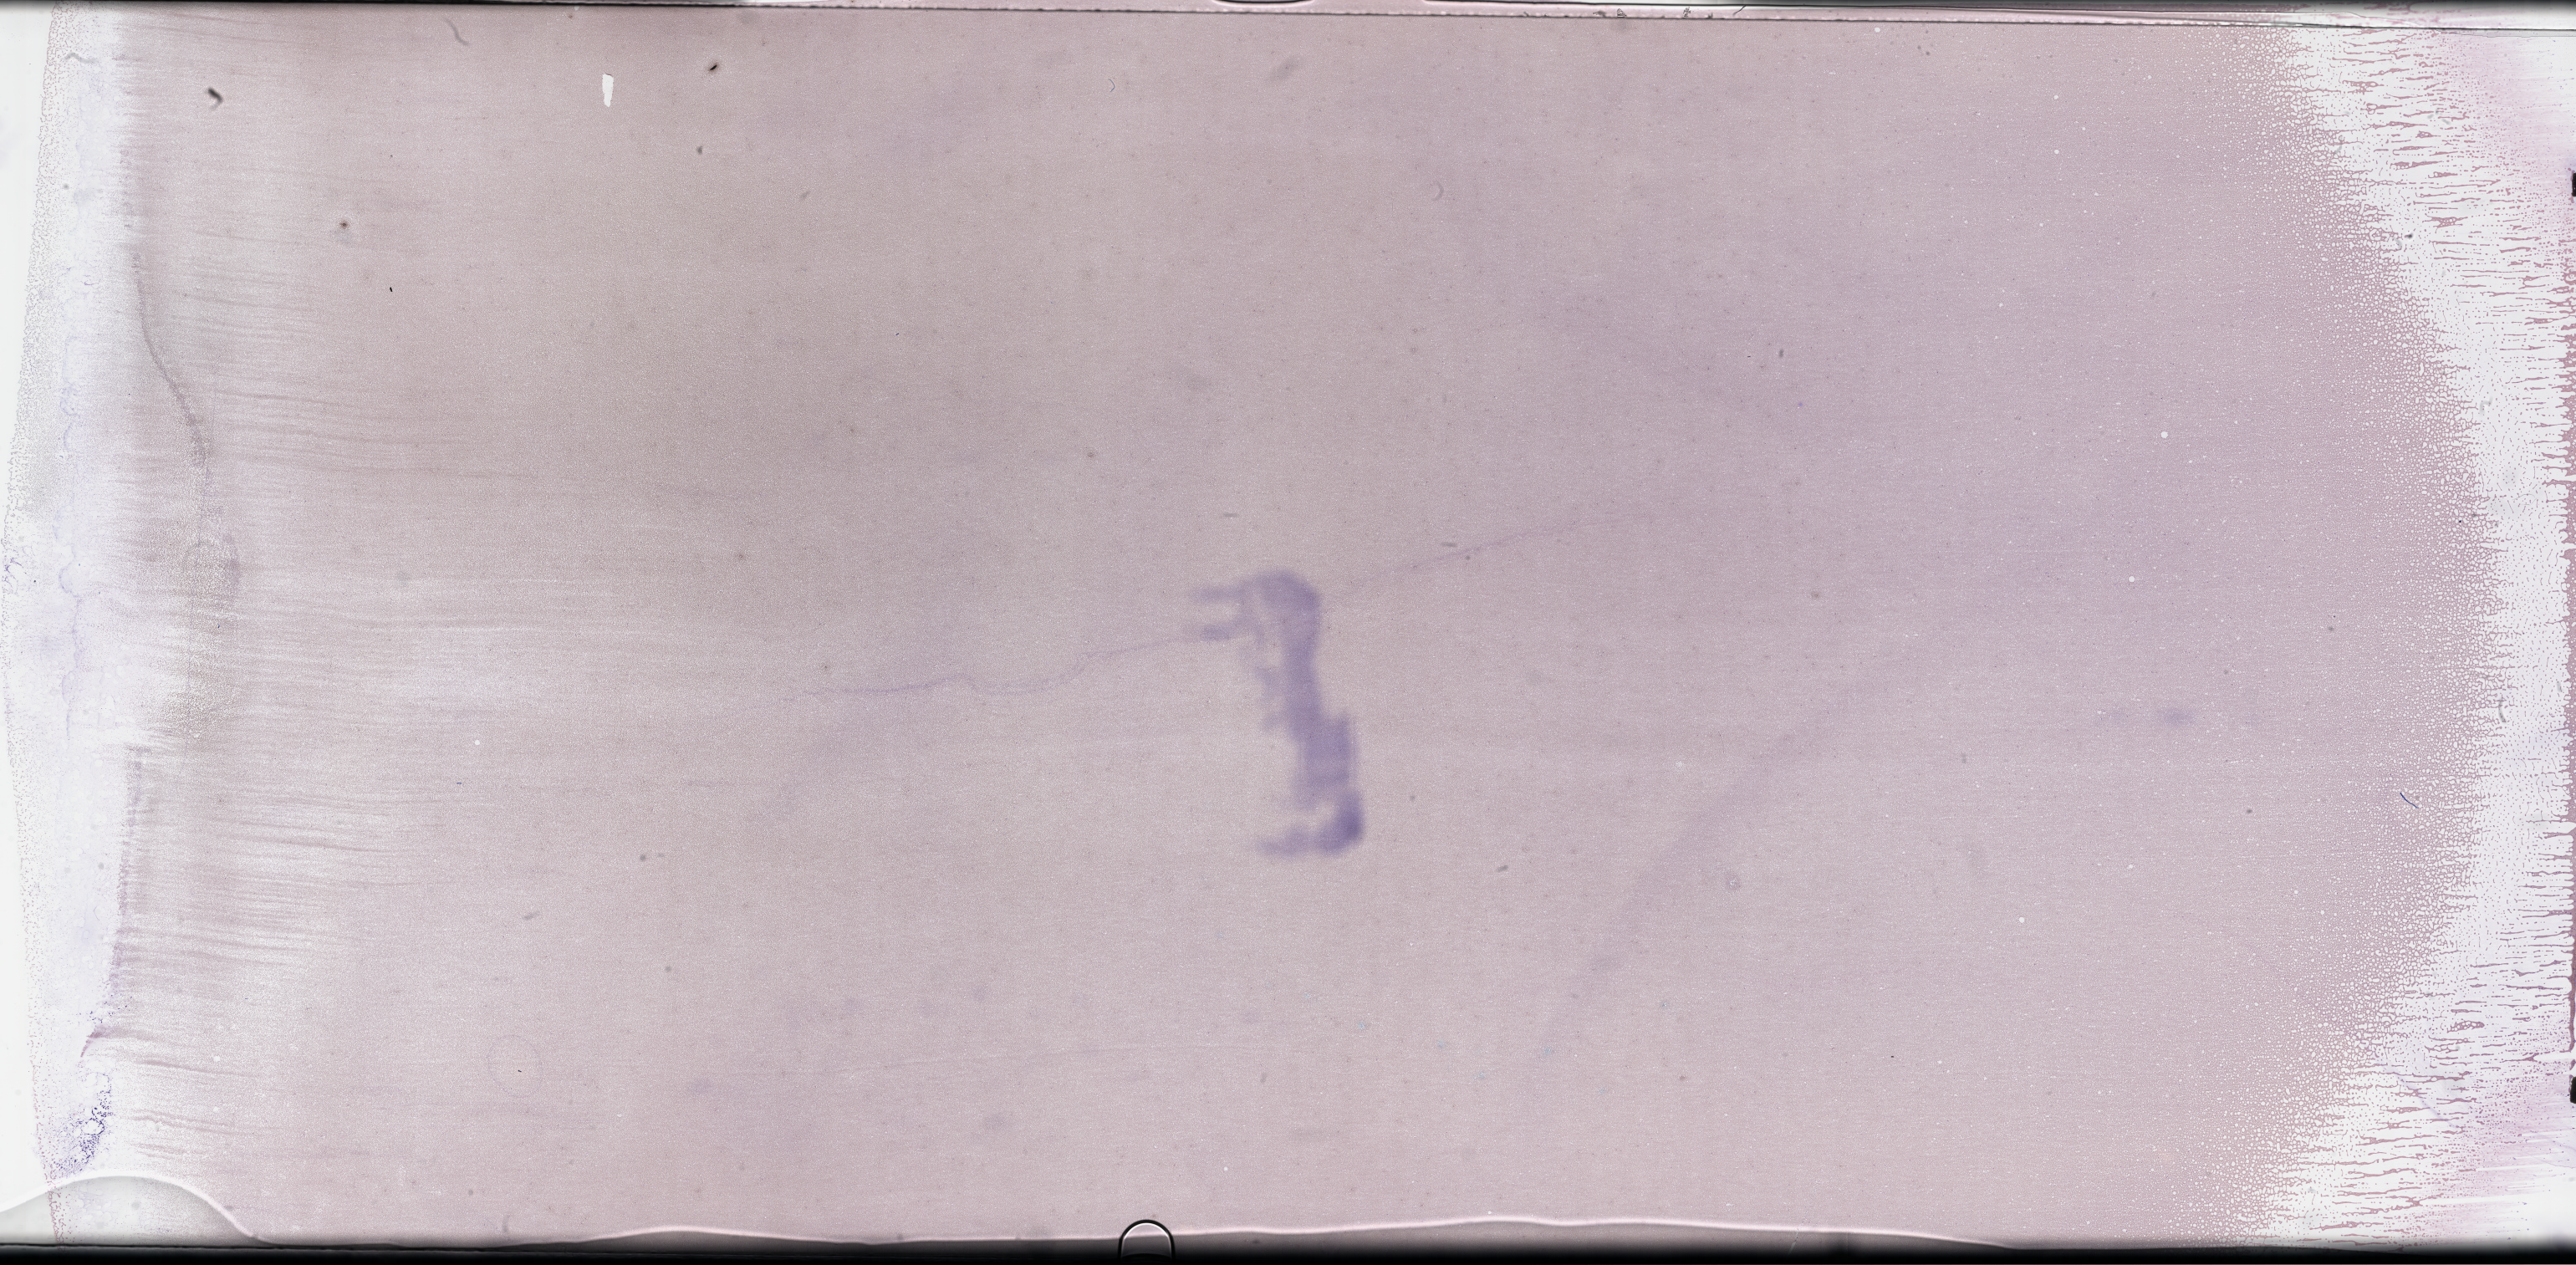
Wright-Giemsa-stained whole blood smear, whole-slide image, shown as a low-resolution overview of the whole scanned area (about 49.8 x 24.4 mm). Patient: male.
- patient diagnosis: Plasma Cell Myeloma